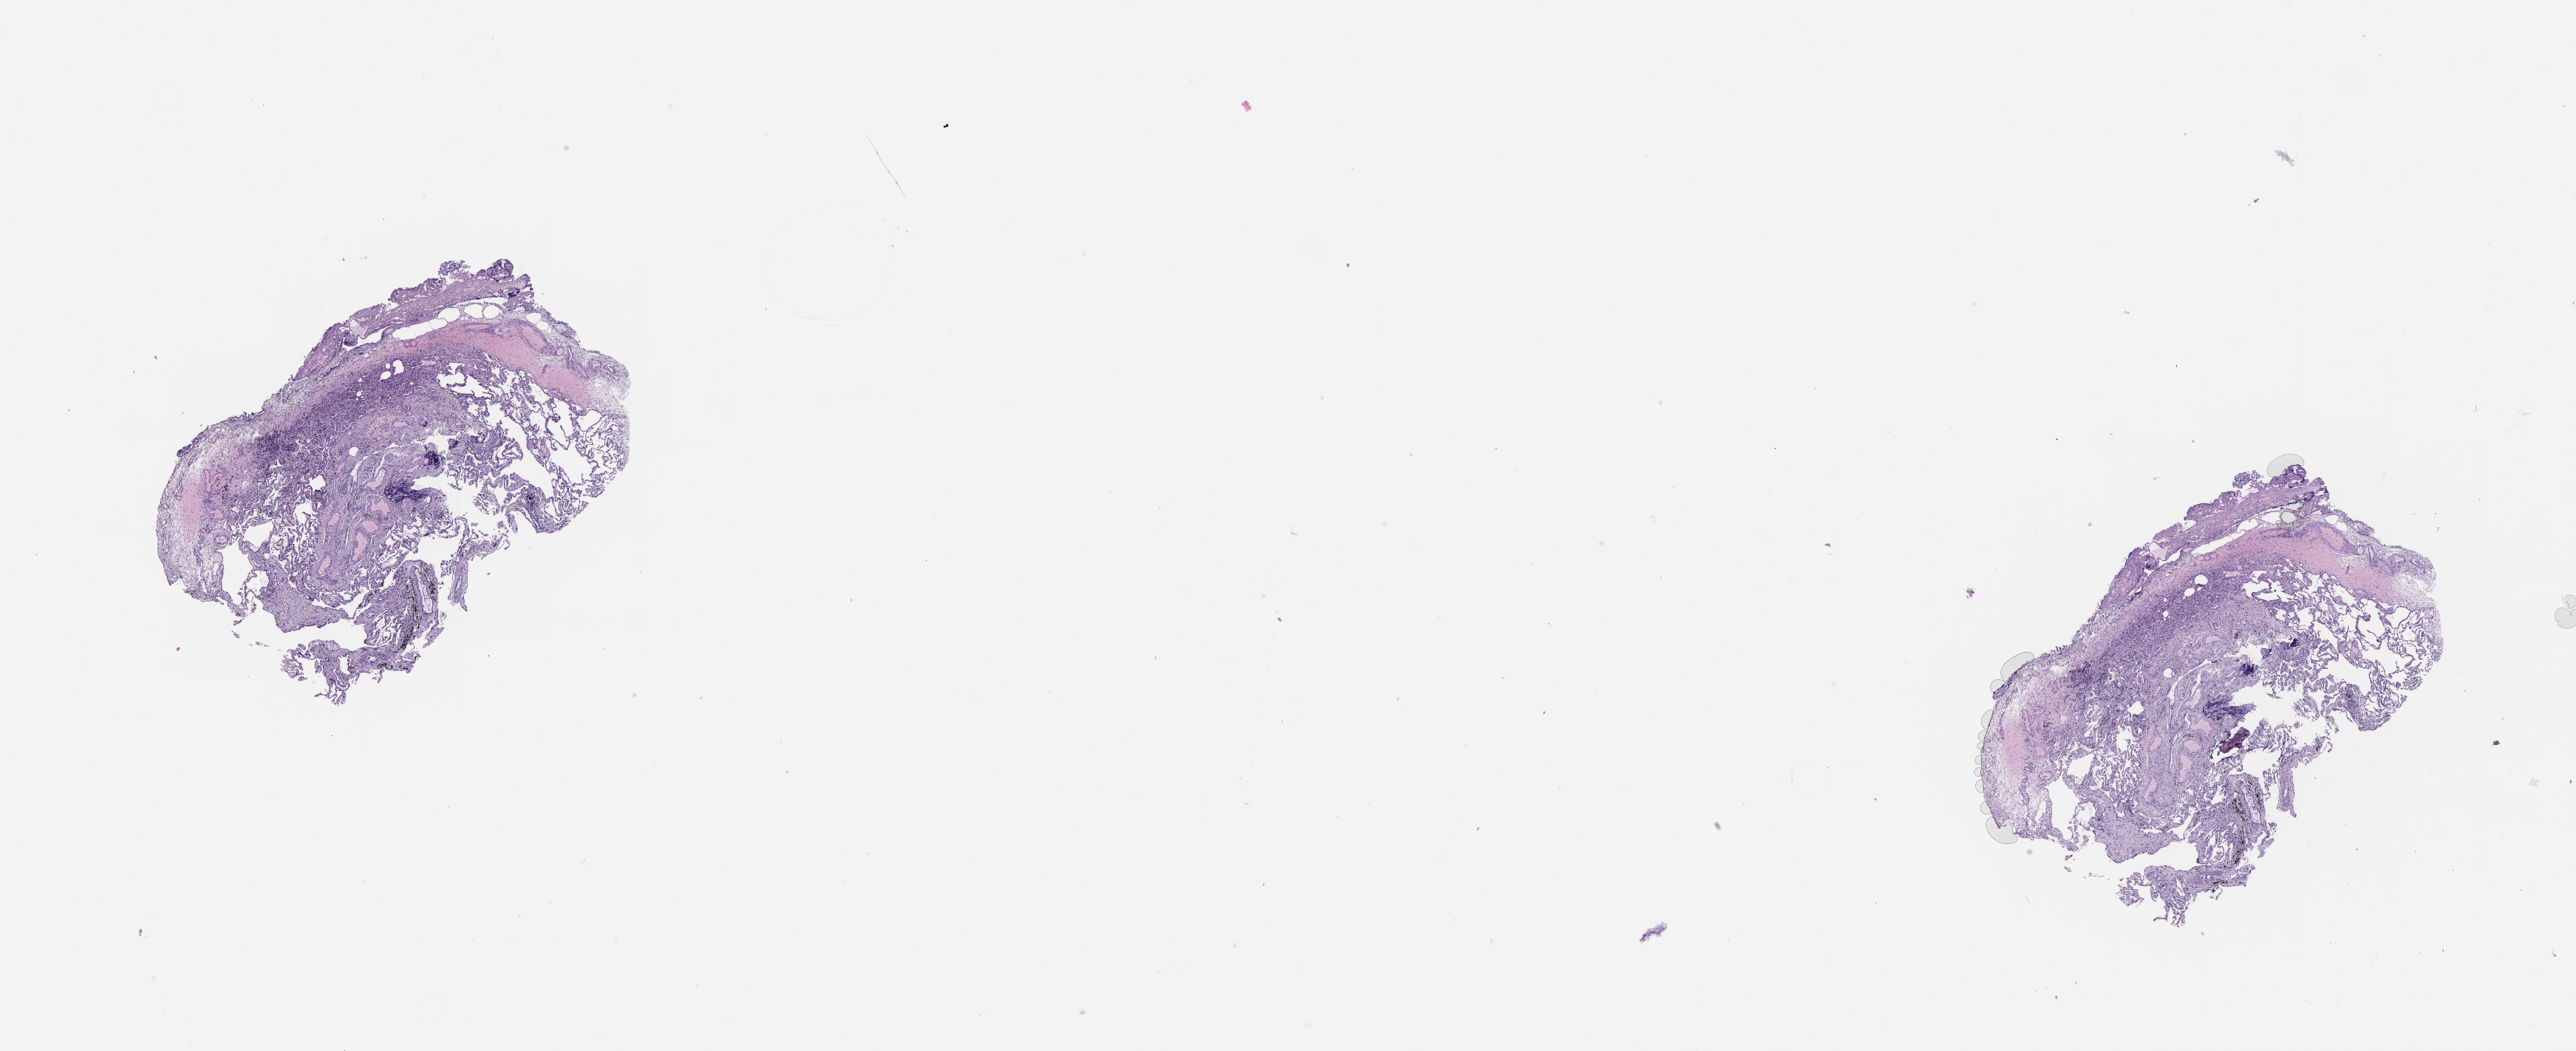
H&E-stained whole-slide image — whole scanned area (about 28.1 x 11.4 mm) shown as a low-resolution overview. Normal (non-tumour) tissue sample, lung. Male, 63 y/o.
This section: normal (non-tumour) tissue from the same patient. Patient diagnosis (cohort enrolment): squamous cell carcinoma (lung).